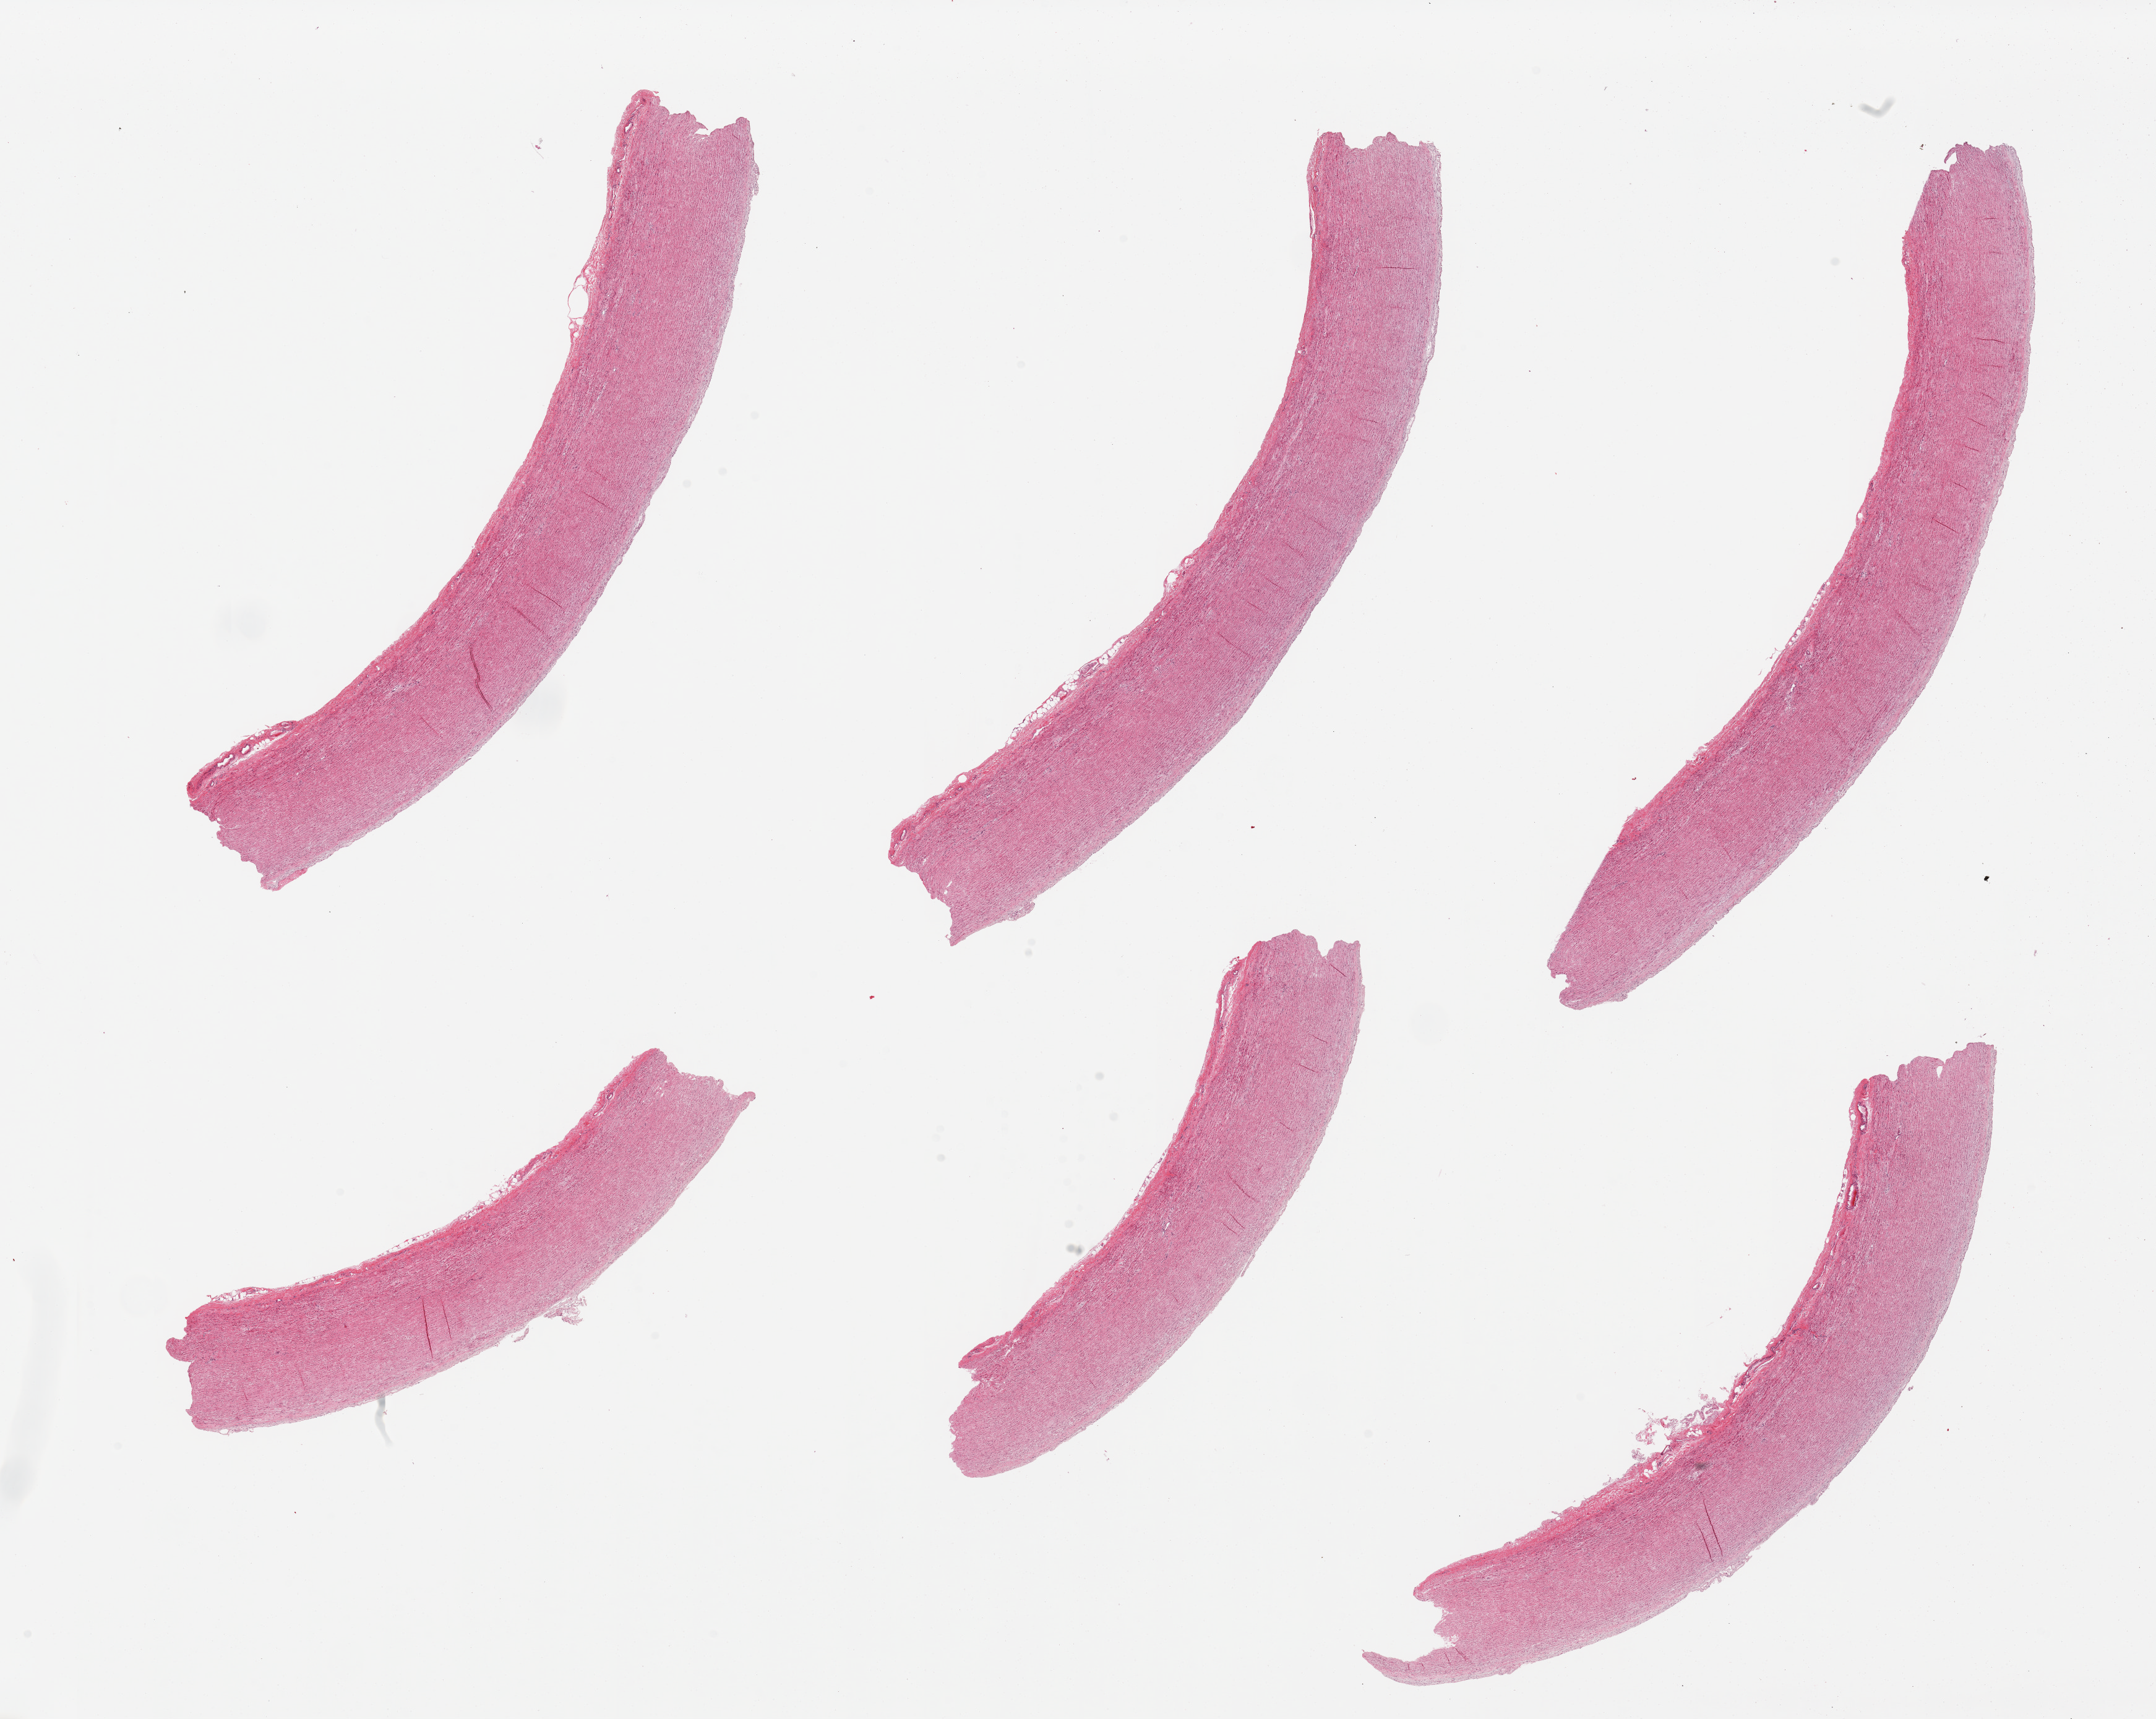
Whole-slide image, haematoxylin and eosin stain, brightfield — shown as a low-resolution overview of the whole scanned area (about 27.6 x 22.0 mm). PAXgene-fixed, paraffin-embedded tissue. Target tissue: aorta. Tissue donor sample. Donor sex: female.
Reviewer comment on this tissue sample: 6 pieces; well trimmed; no plaques.